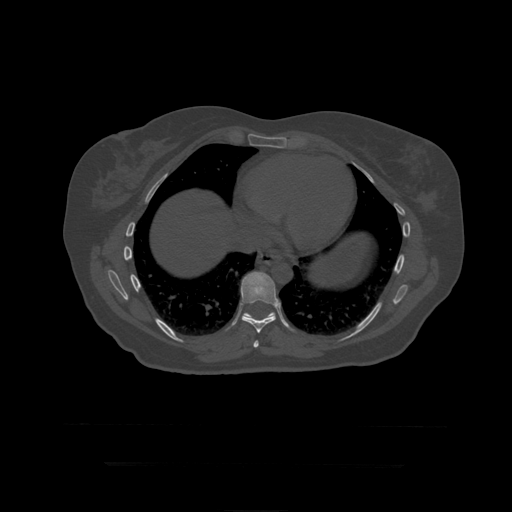
CT including the spine, one axial slice; position 257 of 399 along the scan axis; reconstruction kernel STANDARD; bone window (W 1800 / L 400 HU); 1.25 mm slice thickness; 512 × 512 image matrix, field of view 450 × 450 mm. Patient age 41 years. From the clinical record (not read from this slice): primary cancer: breast.
Annotated regions visible in this slice (semi-automatic segmentation, software-assisted and operator-edited):
- T10 vertebra: bounding box <243,313,275,319> (left, top, right, bottom; pixels)
- T8 vertebra: <253,340,259,348>
- T9 vertebra: <241,272,281,334>